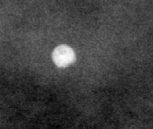
Cropped region of a digitized screen-film mammogram centred on a radiologist-marked abnormality; right breast; CC view; BI-RADS breast density category 4 (scale 1–4).
Marked abnormality: calcifications, morphology round and regular / lucent center / punctate, distribution diffusely scattered; BI-RADS assessment category 2; subtlety rating 5 on a 1 (subtle) to 5 (obvious) scale; benign without callback (not worked up further).